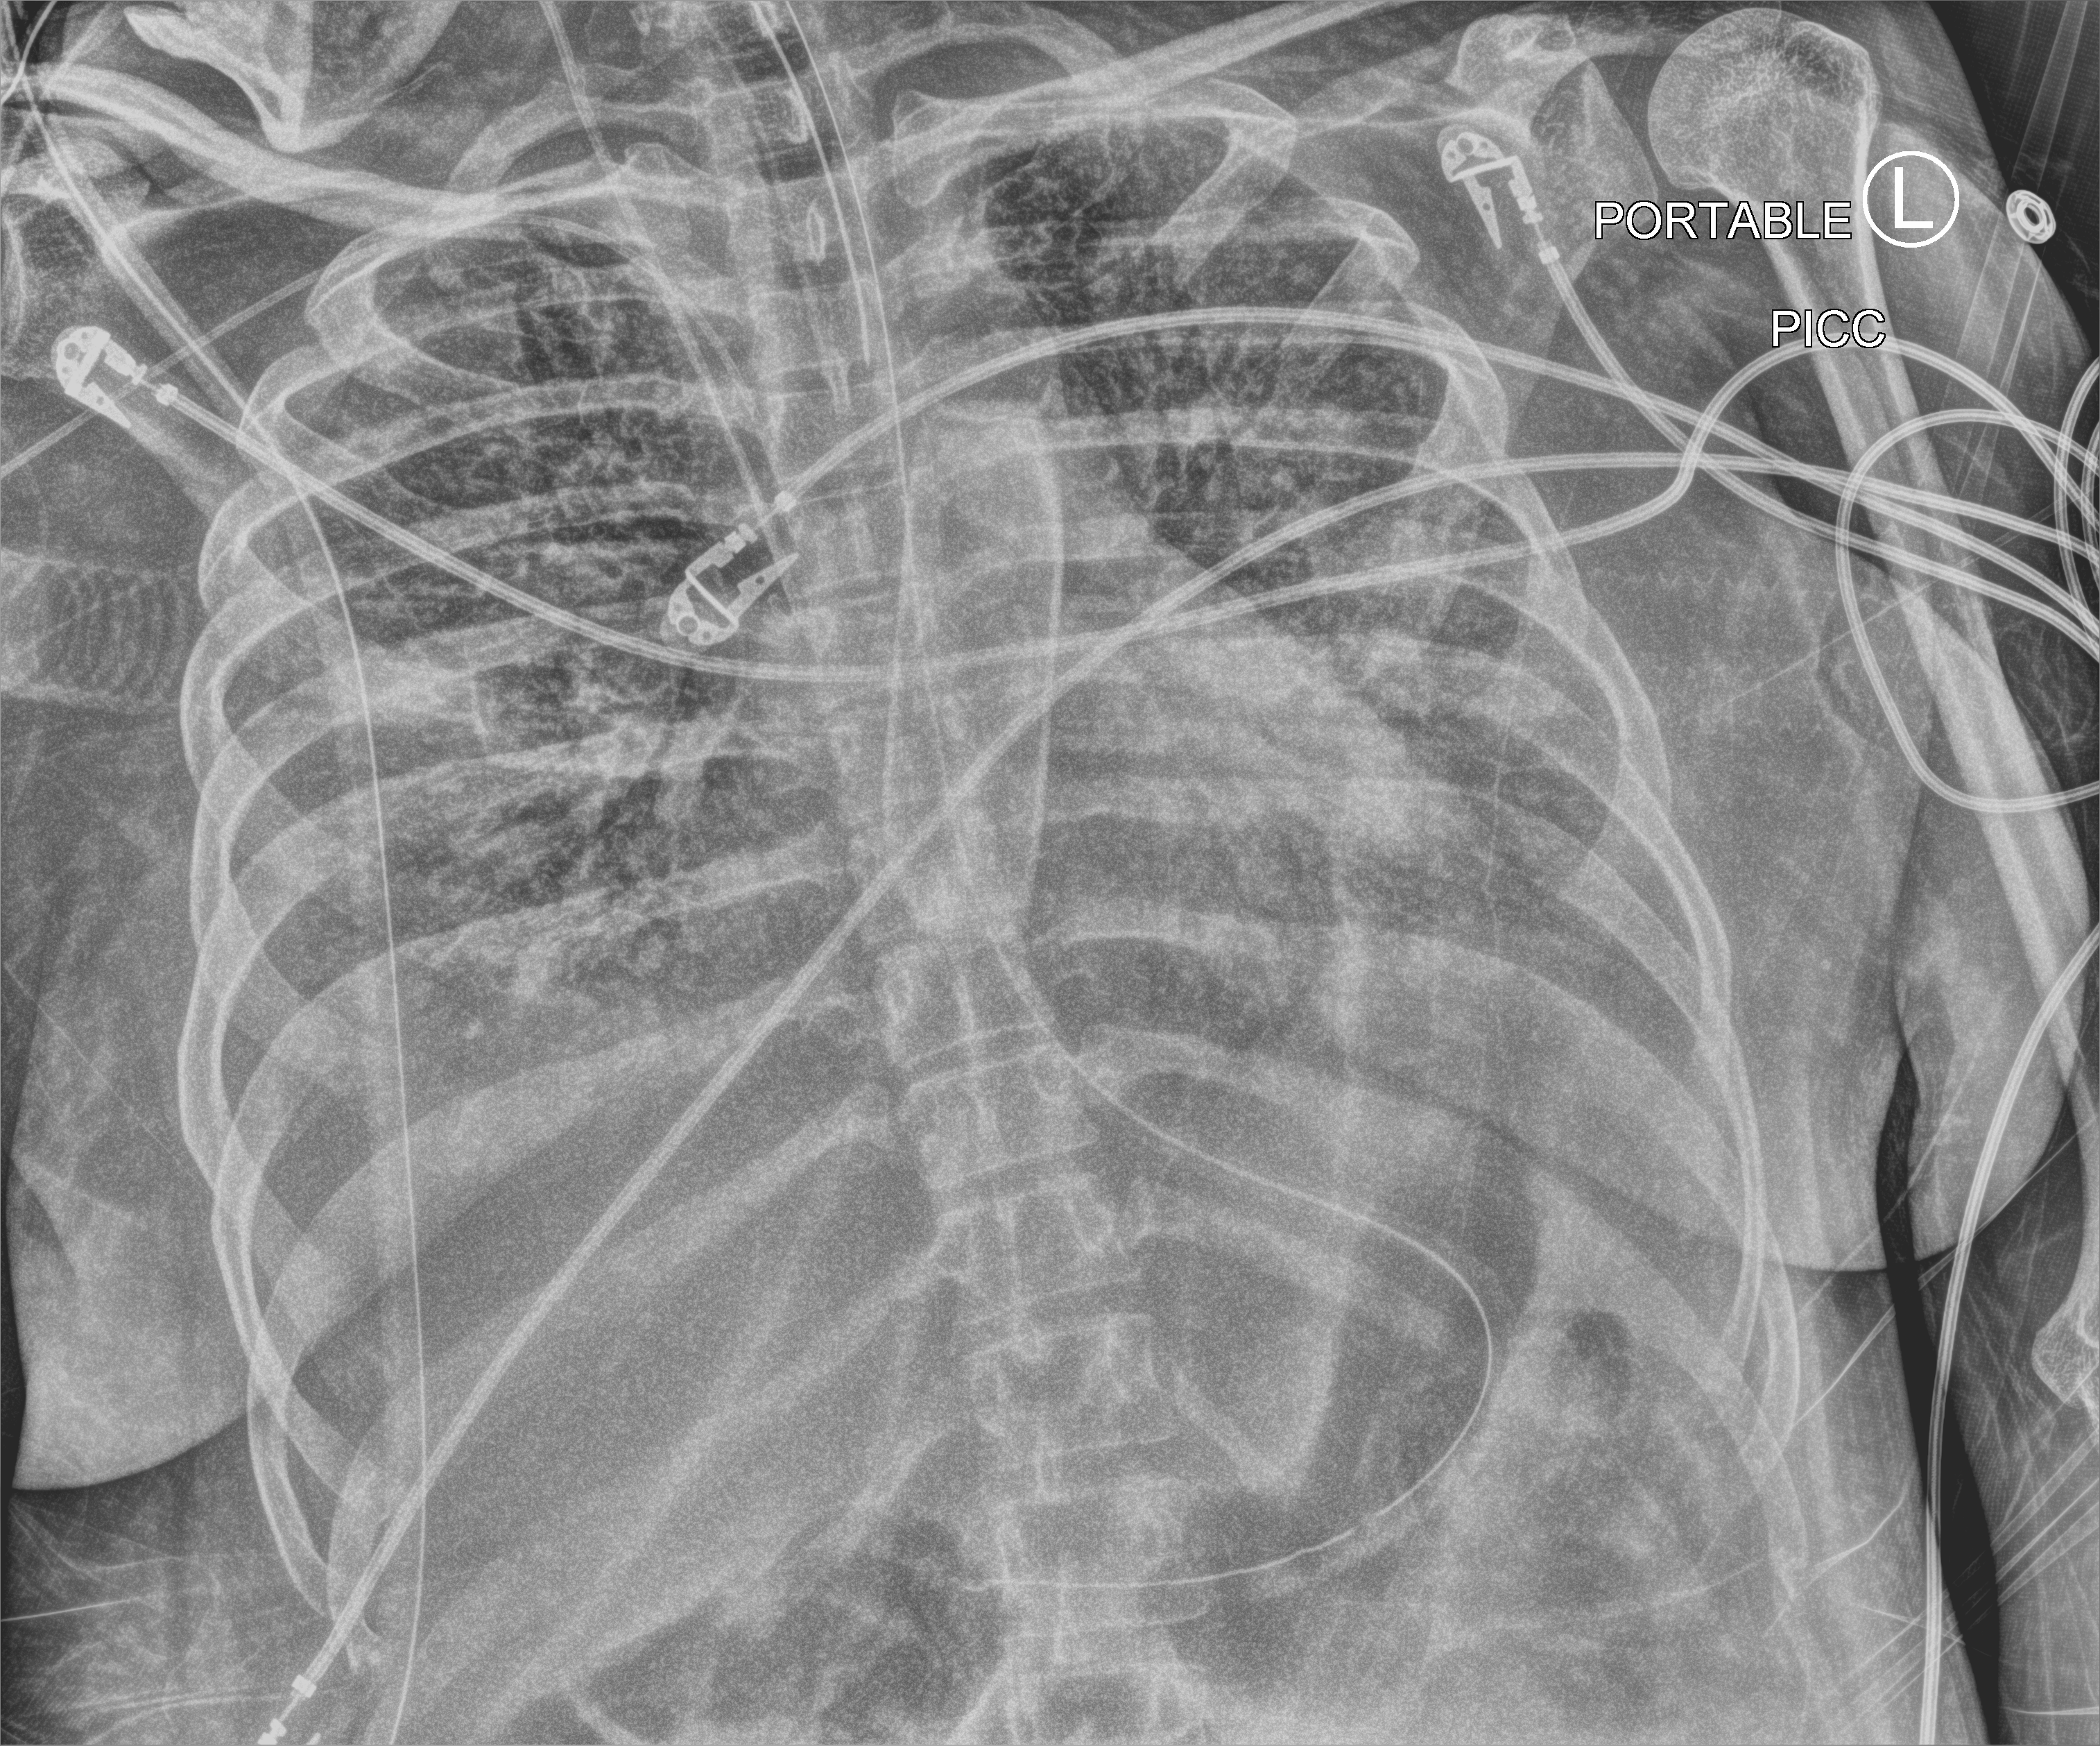
Bedside chest radiograph (computed radiography), anteroposterior (AP) projection. Adult patient hospitalised with COVID-19, age 18–59 years.
From the hospital-stay record, not from the radiograph (when in the stay this image was taken is not recorded): other chronic lung disease (admission record): no; length of hospital stay: 15 days.